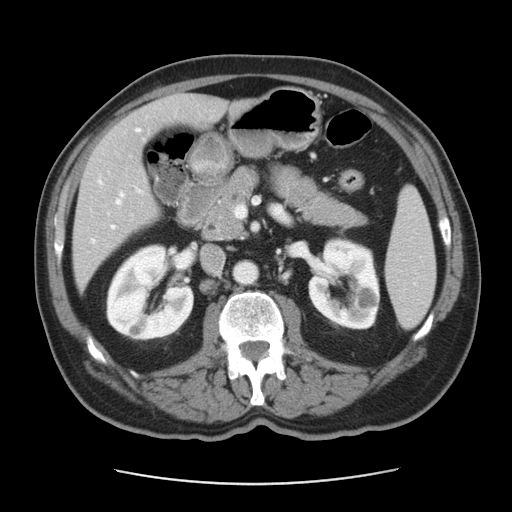
Contrast-enhanced abdominal CT, one axial slice; position 20 of 42 along the scan axis; reconstruction kernel STANDARD; 120 kVp; soft-tissue window (W 400 / L 40 HU); 512 × 512 image matrix, field of view 370 × 370 mm. Male patient, age 73 years. From the clinical record (not read from this slice): diagnosis: colorectal cancer liver metastases, imaged before liver resection; multiple liver metastases: yes; largest metastasis: 0.5 cm; chemotherapy before resection: yes.
Outlined on this slice (expert manual segmentation):
- hepatic veins: bounding box <90,129,139,244> (left, top, right, bottom; pixels)
- liver: <74,95,226,287>
- planned liver remnant (the part of the liver to remain after resection): <111,95,226,161>
- portal vein (with intrahepatic branches): <111,225,115,229>